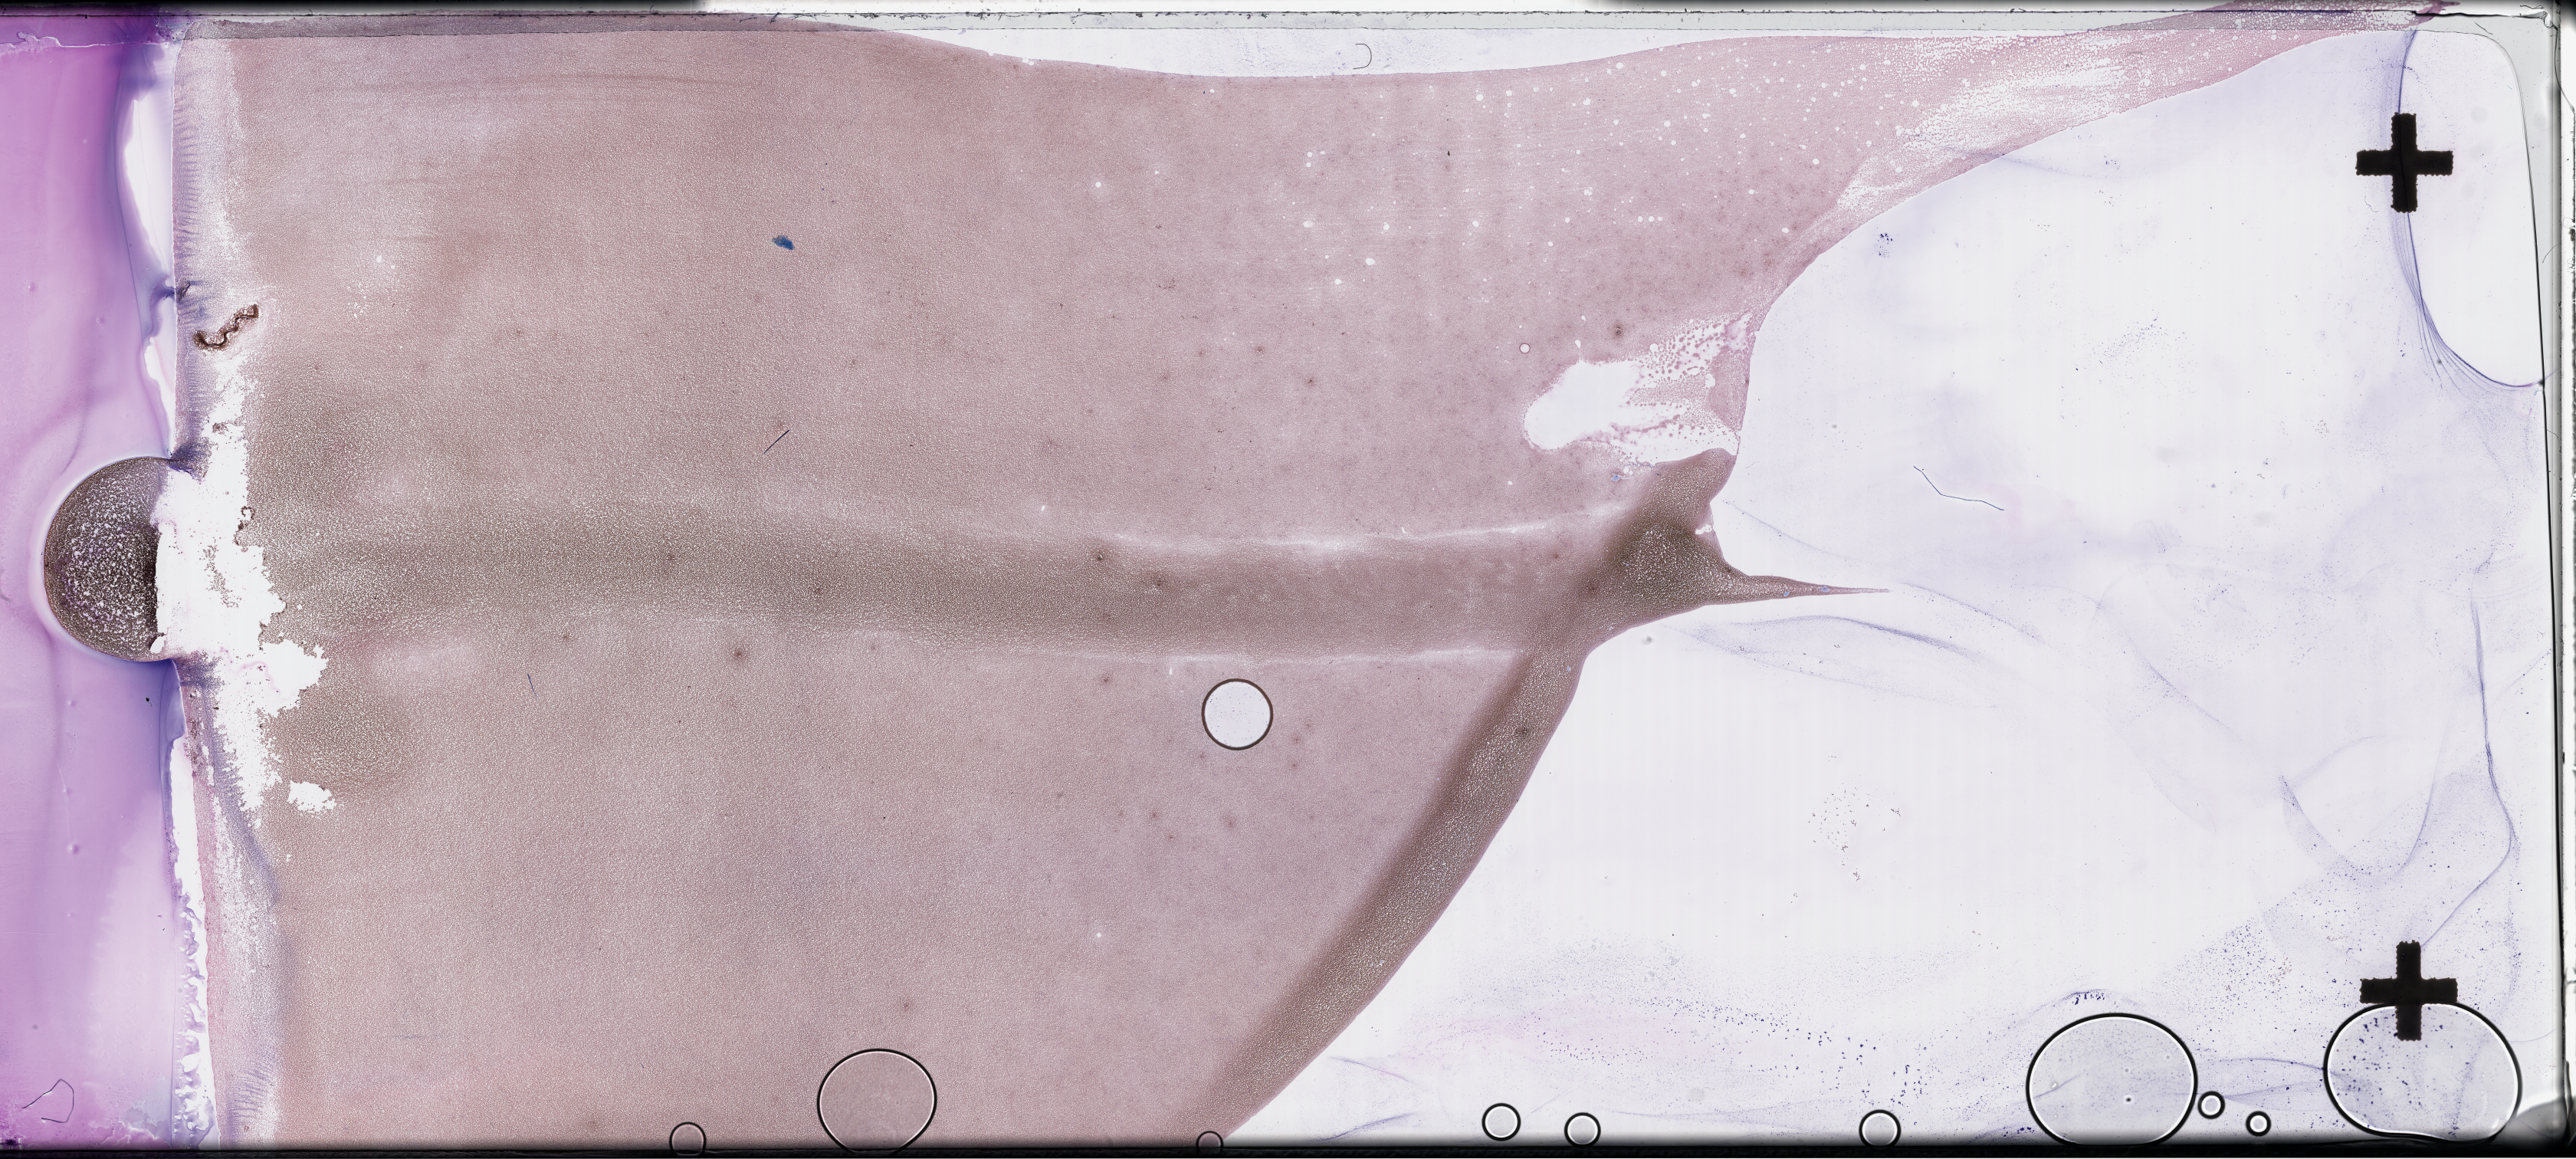
Wright–Giemsa-stained whole blood smear, whole-slide image, a low-resolution overview of the entire scanned area, about 54.3 x 24.4 mm, specimen time point: collected on treatment. Patient: female.
From a patient with: Plasma Cell Myeloma.